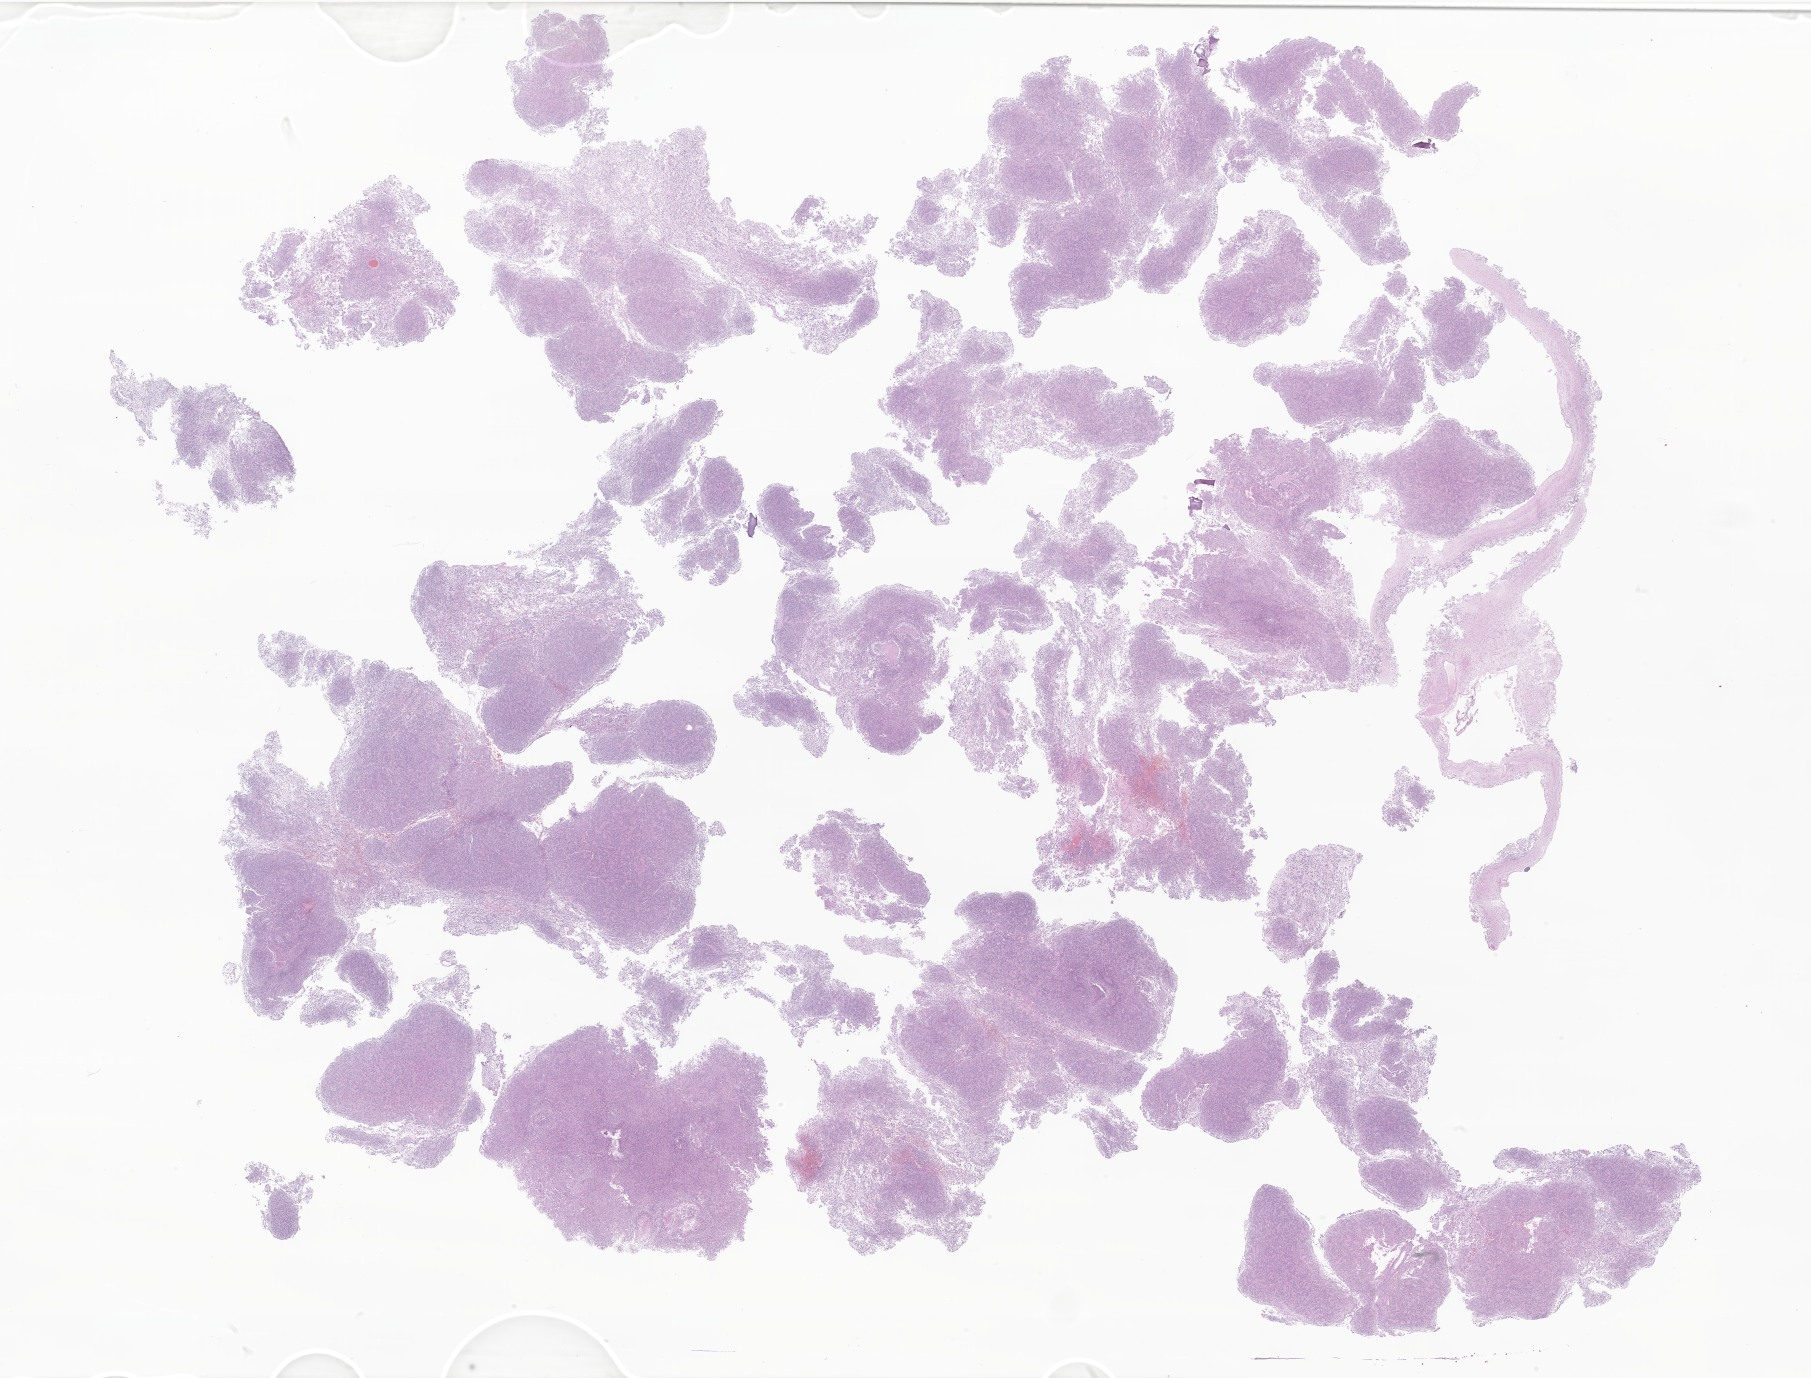
Whole-slide image, hematoxylin and eosin (H&E) stain of tumor tissue from the brain, low-resolution overview of the scanned area, about 30.5 x 23.2 mm. Formalin-fixed paraffin-embedded section. Female patient, age 171 days.
• diagnosis (ICD-O-3 morphology term): Ependymoma, NOS